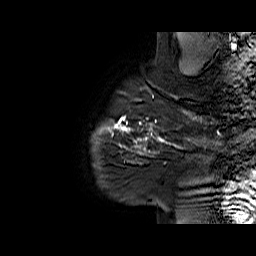
Breast MRI (dynamic contrast-enhanced), one sagittal slice; position 57 of 60 along the scan axis; dynamic contrast-enhanced series, time point 2 of 6 at this slice position (early post-contrast); 1.5 T; TE 6.1 ms, TR 32.9 ms; 4 mm slice thickness; 256 × 256 image matrix. Female patient. From the clinical record (not read from this slice): setting: breast cancer imaged before/during neoadjuvant chemotherapy; receptor status: HER2-positive.
Annotated regions visible in this slice (semi-automatically segmented with operator editing):
- analysis volume of interest (the breast-tissue region the enhancement analysis was run in; not a lesion): bounding box <127,95,194,165> (left, top, right, bottom; pixels)
- tumour enhancement mask (voxels above the 100 % enhancement threshold inside the analysis volume of interest): <127,95,194,155>